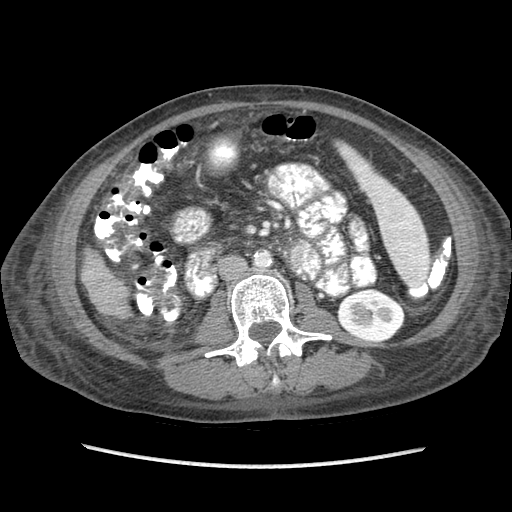
Contrast-enhanced abdominal CT (liver protocol), one axial slice; slice 18 of 87 in the series (ordered by position); reconstruction kernel STANDARD; 120 kVp; soft-tissue window (W 400 / L 40 HU); 512 × 512 image matrix, field of view 340 × 340 mm. From the clinical record (not read from this slice): diagnosis: hepatocellular carcinoma (patient treated with transarterial chemoembolisation; whether this scan precedes or follows treatment is not stated here); TNM stage (as recorded): Stage-IIIB; Child-Pugh class: A.
Annotated regions visible in this slice (semi-automatic segmentation, software-assisted and operator-edited):
- liver parenchyma outside the tumour (the mass and vessels are separate outlines, so this box may not span the whole liver): bounding box [x1, y1, x2, y2] px = [82, 248, 128, 314]